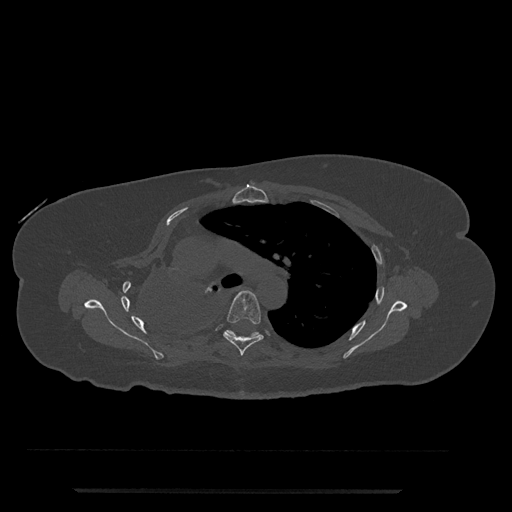
CT including the spine, one axial slice; position 536 of 797 along the scan axis; bone window (W 1800 / L 400 HU); 0.5 mm slice thickness; 512 × 512 image matrix, field of view 440 × 440 mm. Patient: female, 51 years. From the clinical record (not read from this slice): primary cancer: neuro.
Outlined on this slice (semi-automatically segmented with operator editing):
- T5 vertebra: bounding box [x1, y1, x2, y2] px = [223, 290, 264, 356]
- T6 vertebra: [225, 330, 260, 338]